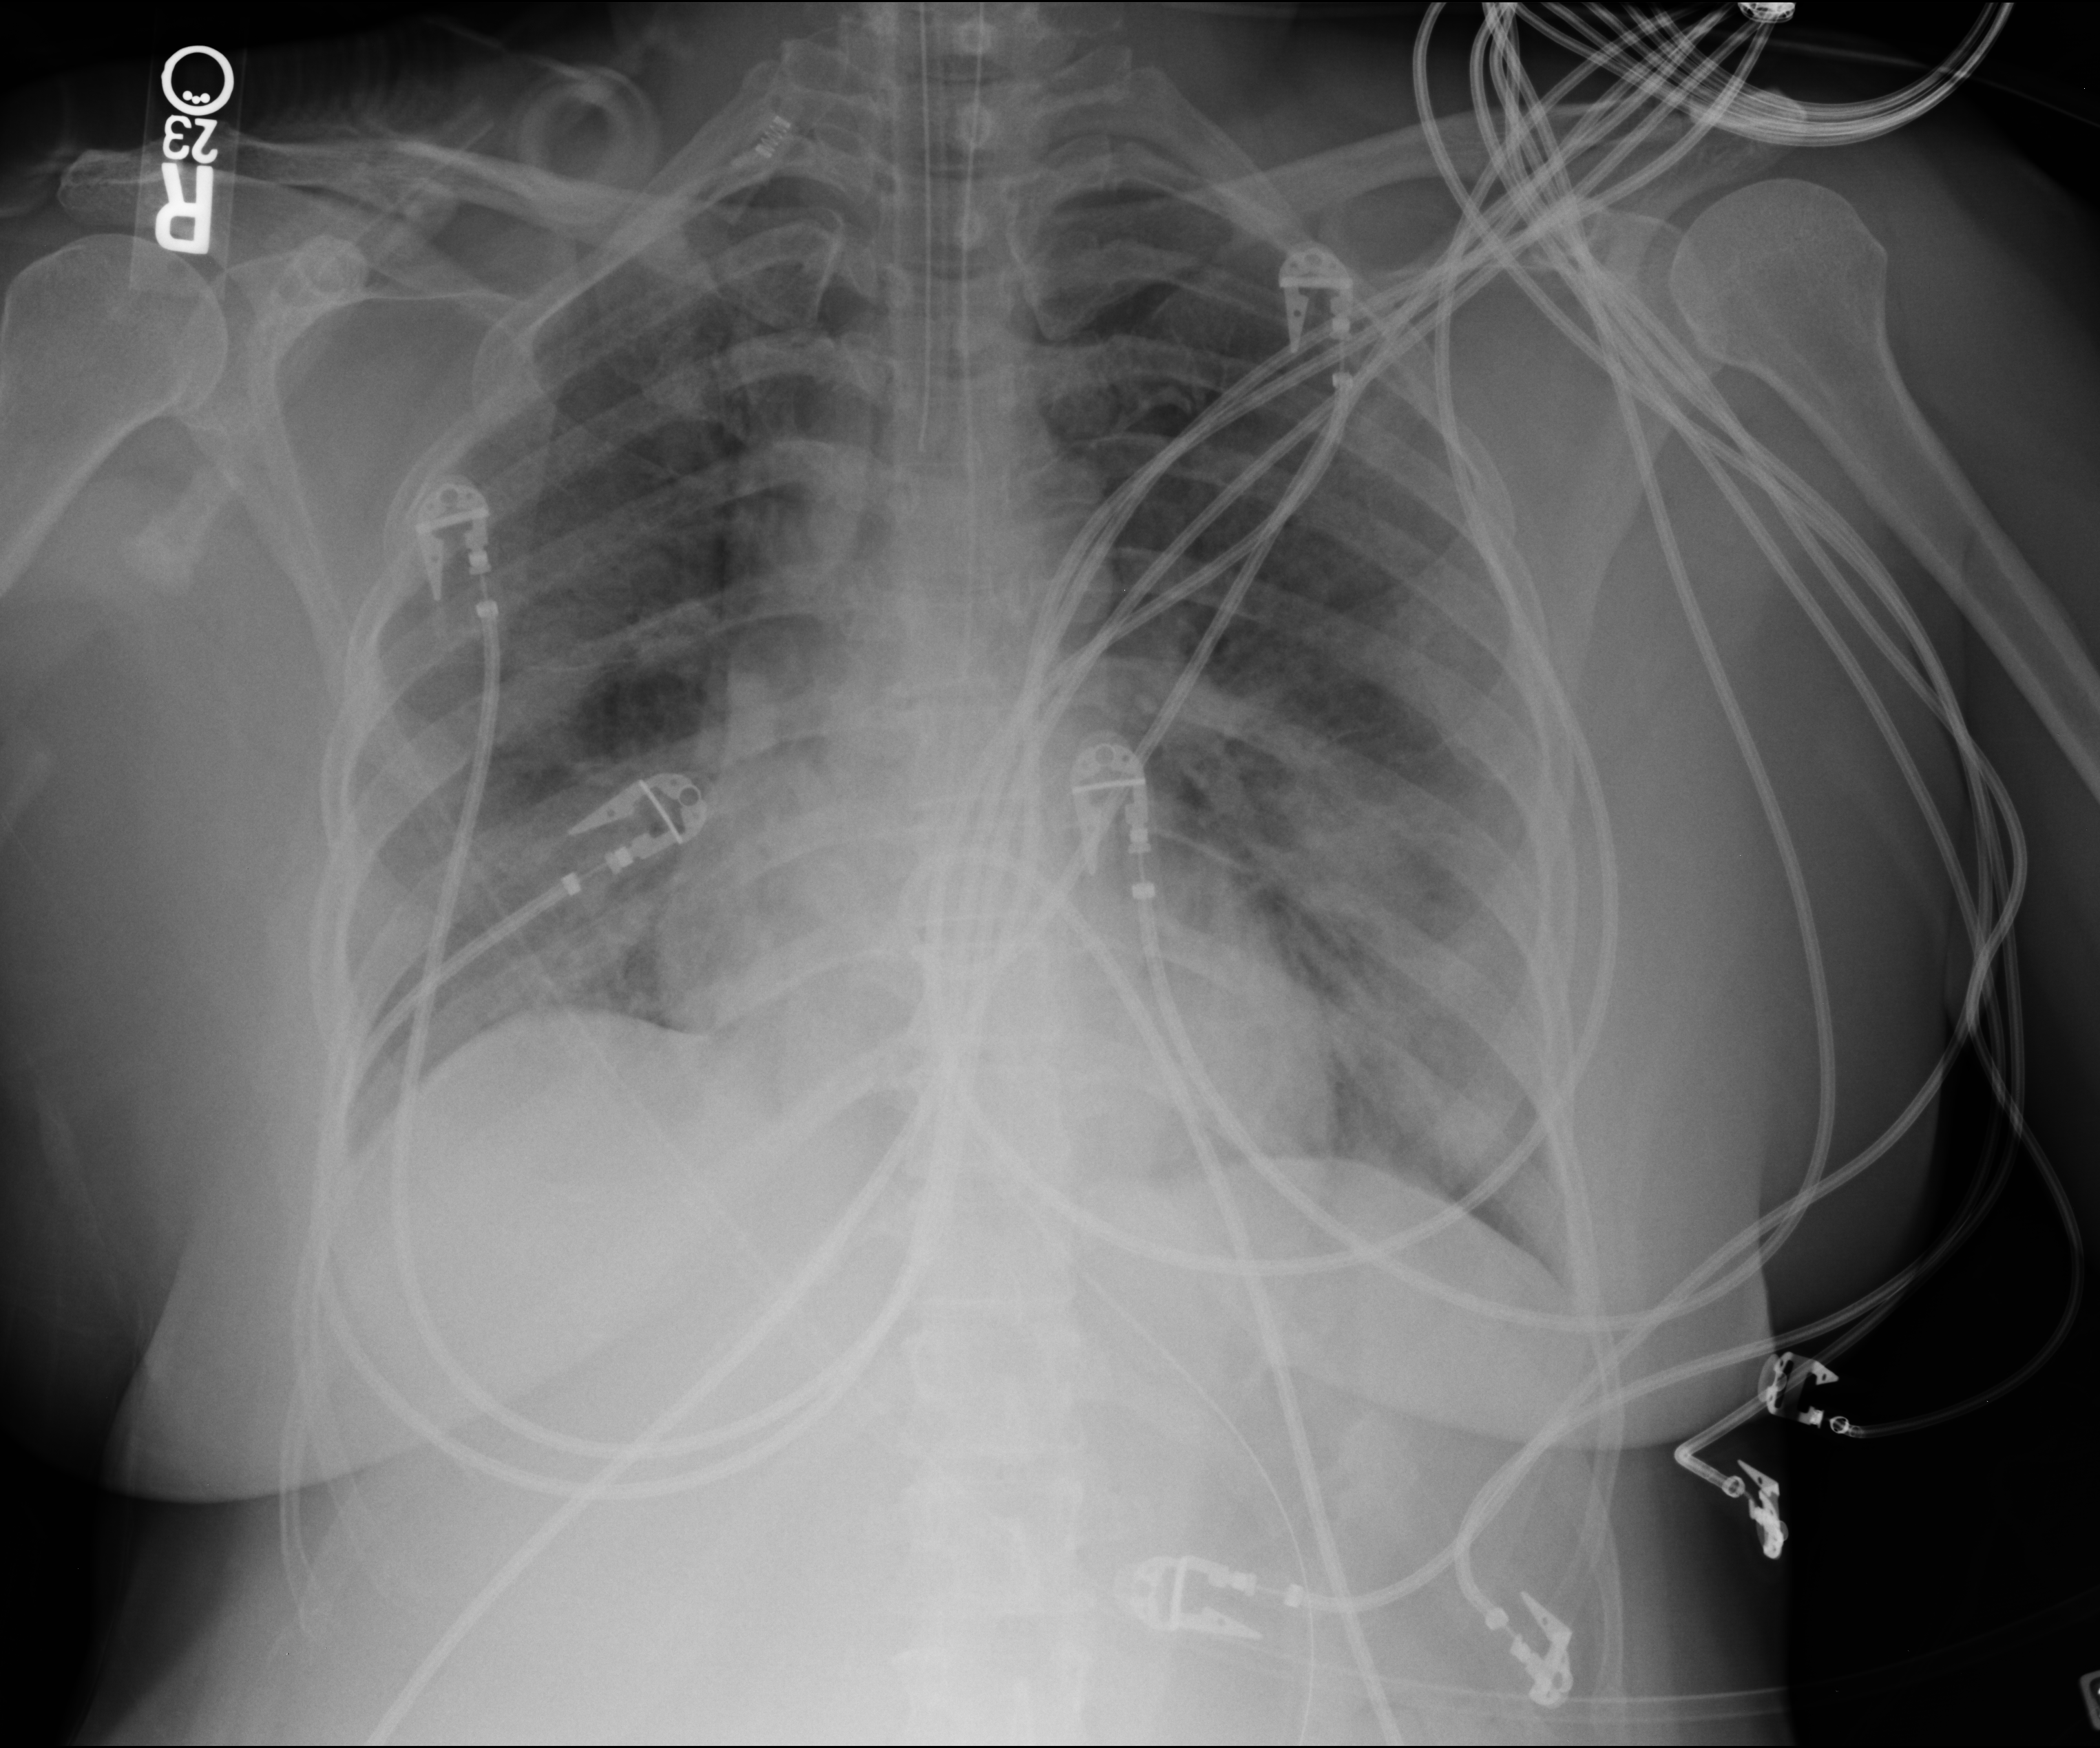
Portable chest radiograph, anteroposterior (AP) projection. Patient hospitalised with COVID-19; male, aged 18–59 years.
Hospital-stay facts (about this admission, not read from this image; timing relative to this image not recorded):
- admitted to intensive care during this hospital stay: yes